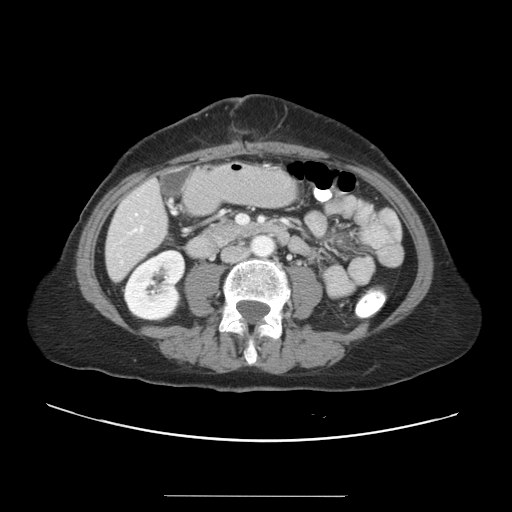
Contrast-enhanced abdominal CT, one axial slice; position 6 of 34 along the scan axis; reconstruction kernel STANDARD; 120 kVp; intravenous contrast given; soft-tissue window (W 400 / L 40 HU); 5 mm slice thickness; 512 × 512 image matrix, field of view 382 × 382 mm. Female patient, age 69 years. From the clinical record (not read from this slice): diagnosis: colorectal cancer liver metastases, imaged before liver resection; multiple liver metastases: yes; largest metastasis: 1.4 cm.
Annotated regions visible in this slice (outlined manually by an expert reader):
- liver: bounding box <106,181,167,279> (left, top, right, bottom; pixels)
- planned liver remnant (the part of the liver to remain after resection): <106,229,164,279>
- portal vein (with intrahepatic branches): <131,216,248,233>